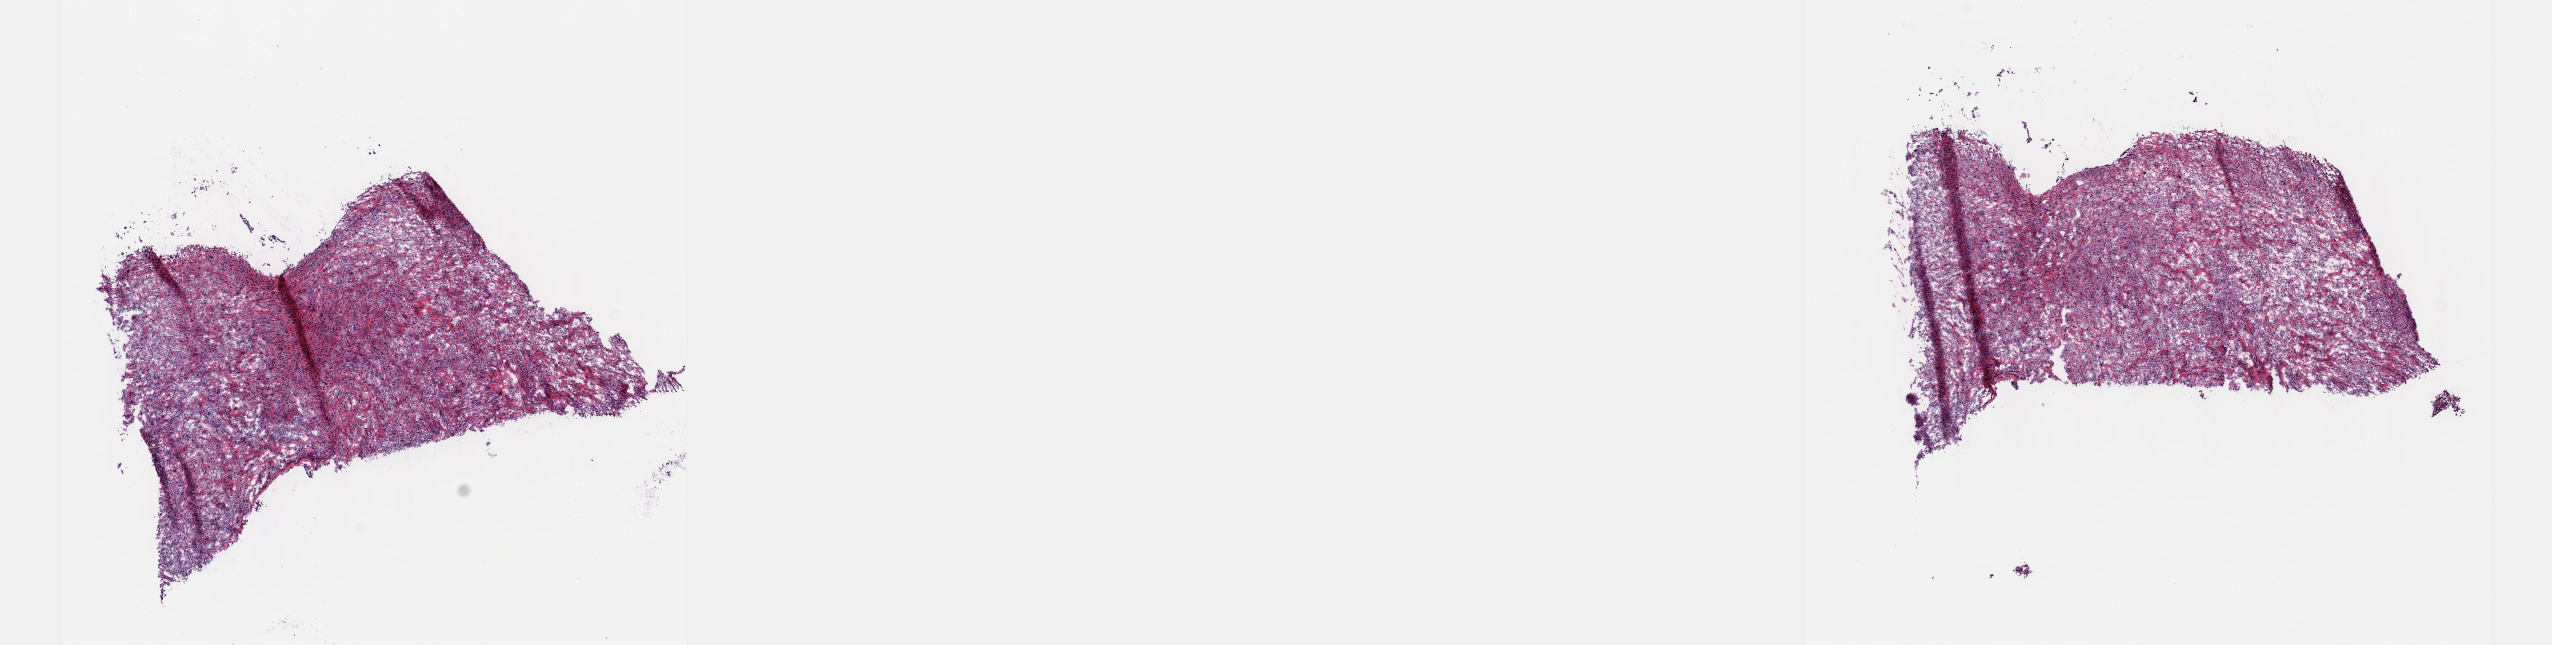
Hematoxylin and eosin (H&E) stained whole-slide image — shown as a low-resolution overview of the whole scanned area (about 20.6 x 5.2 mm, from a 40x scan), frozen section, primary tumour sample from the liver. Male patient; age at initial diagnosis 56 years.
Histologic diagnosis: Hepatocellular carcinoma, NOS.